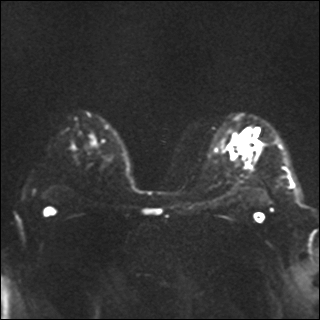
Breast MRI, one axial slice. Slice 21 of 35 in the series (ordered by position). Diffusion-weighted series; image 2 of 4 stored at this slice position (different b-values; order by instance number). 1.5 T. 4 mm slice thickness. 320 × 320 image matrix, field of view 320 × 320 mm. Female patient.
Structures marked on this image (outlined manually by an expert reader):
- tumour on diffusion-weighted imaging: bounding box (x1, y1, x2, y2) in pixels: (240, 138, 248, 154)